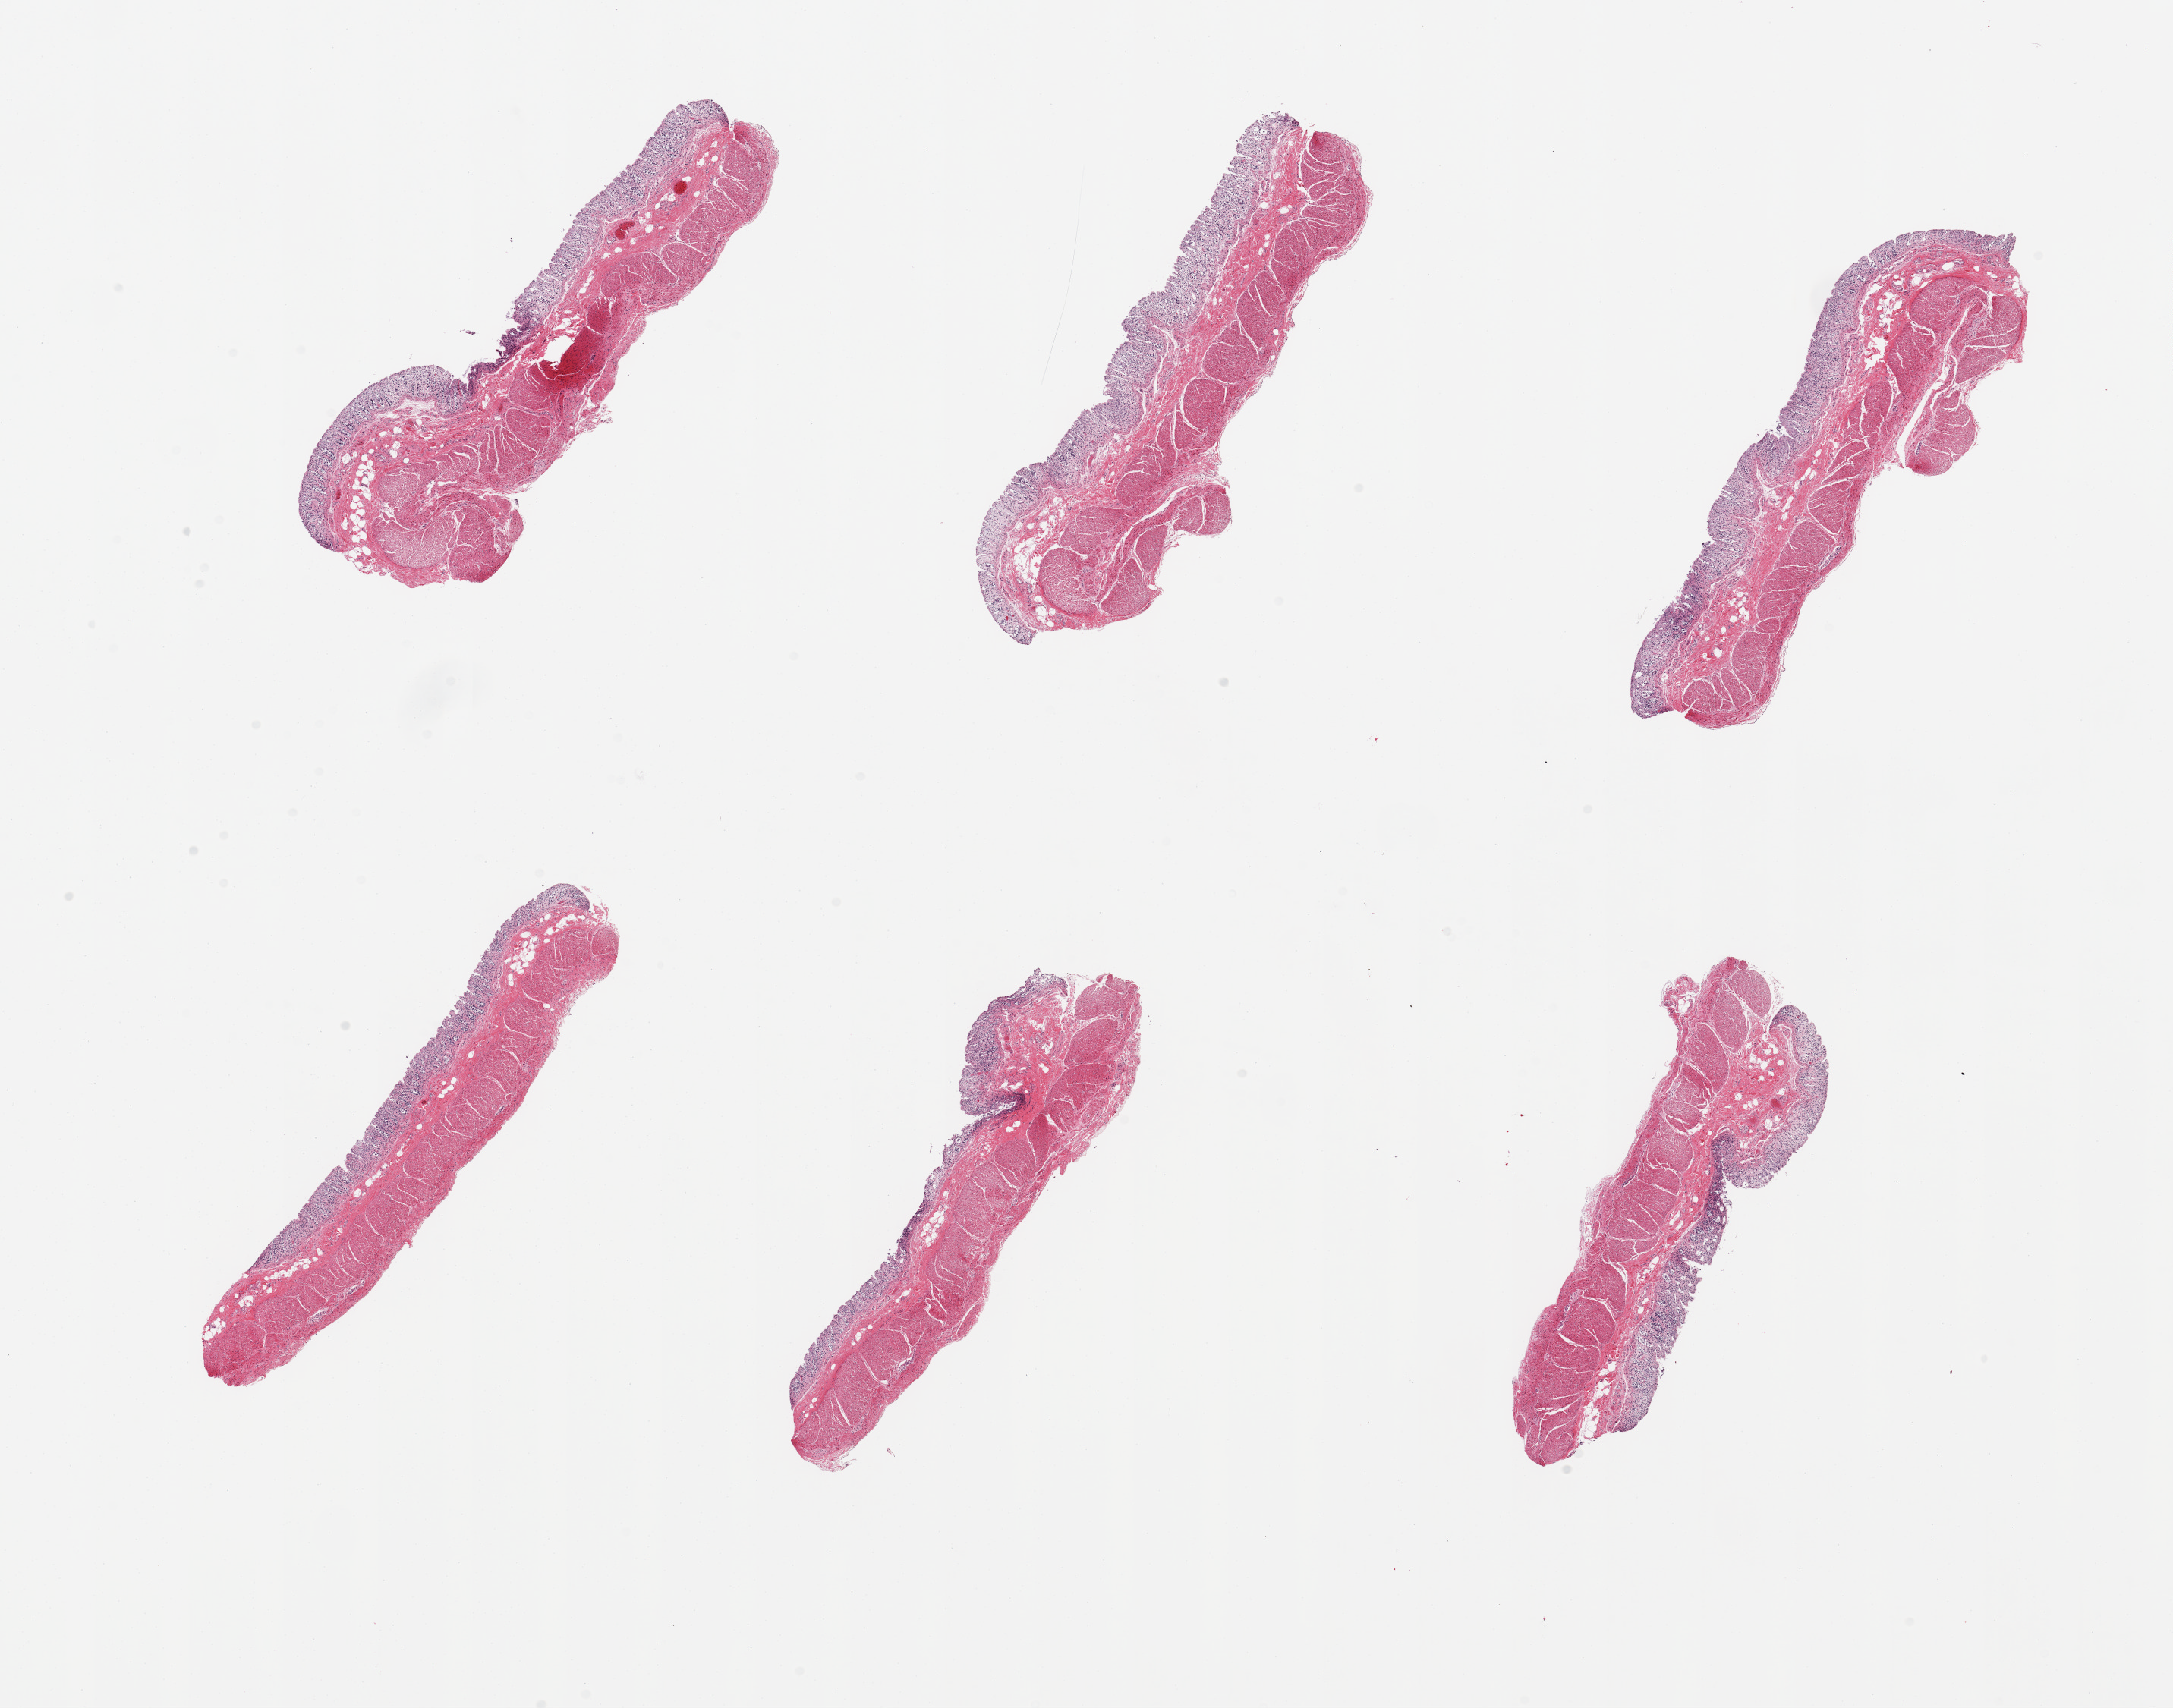
H&E whole-slide image, brightfield, a low-resolution overview of the entire scanned area, about 22.6 x 17.8 mm (slide scanned at 20x). PAXgene-fixed, paraffin-embedded tissue. Sampled site (target tissue): transverse colon. Donor tissue sample.
Pathologist's review note for this sample: 6 pieces; full thickness sections with moderate to severe autolysis (mucosa 3, muscularis 2).